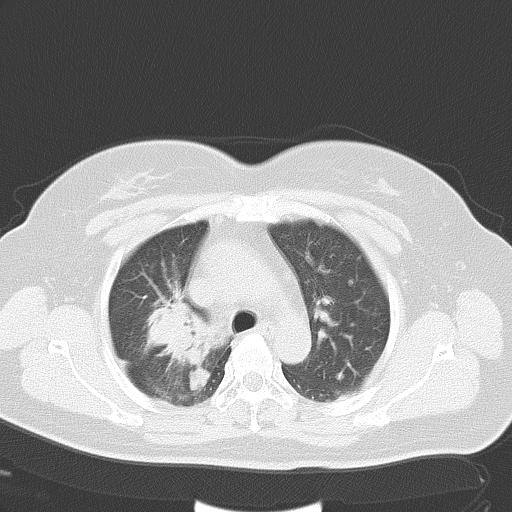
Chest CT, one axial slice. Slice 36 of 48 in the series (ordered by position). 120 kVp. Lung window (W 1500 / L -600 HU). 512 × 512 image matrix, field of view 353 × 353 mm. Female patient, age 50 years. From the clinical record (not read from this slice): clinical TNM (as recorded): T2a N0 M1a.
Outlined on this slice (bounding box drawn by a radiologist):
- lung tumour (recorded histology: adenocarcinoma): bounding box <140,292,219,369> (left, top, right, bottom; pixels)